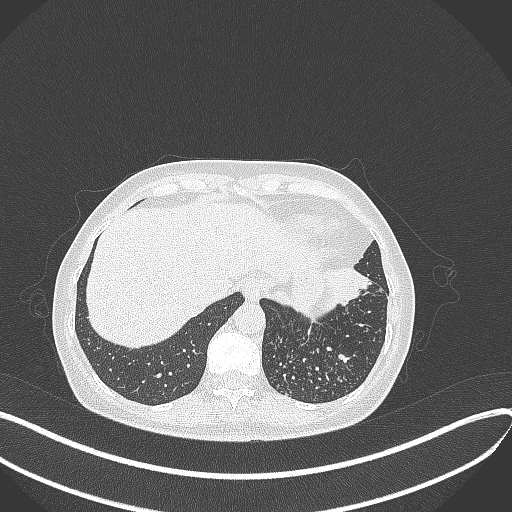
Chest CT, one axial slice. Slice 83 of 429 in the series (ordered by position). Reconstruction kernel B70f. 100 kVp. Lung window (W 1500 / L -600 HU). 1 mm slice thickness. 512 × 512 image matrix, field of view 400 × 400 mm. Female patient, age 63 years. Case-level facts recorded for this patient, not image findings: clinical TNM (as recorded): T1b N0 M0; histopathological grade: G2-3.
Annotated regions visible in this slice (rectangle marked by the reading radiologist):
- lung tumour (recorded histology: adenocarcinoma): bounding box [x1, y1, x2, y2] px = [321, 259, 376, 309]